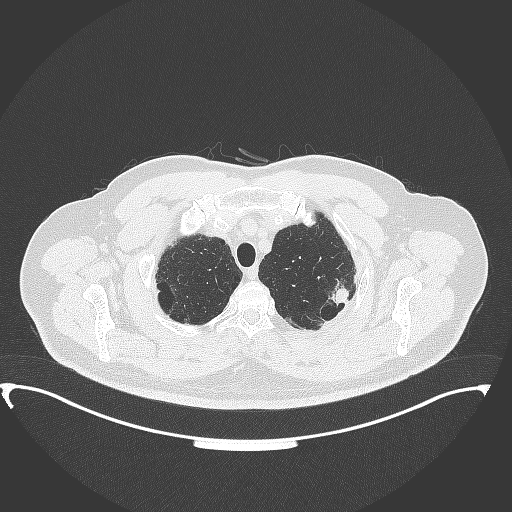
Chest CT, one axial slice. Slice 317 of 350 in the series (ordered by position). 120 kVp. Lung window (W 1500 / L -600 HU). 1 mm slice thickness. 512 × 512 image matrix. Patient: male, 64 years. From the clinical record (not read from this slice): clinical TNM (as recorded): T1c N1 M1.
Structures marked on this image (bounding box drawn by a radiologist):
- lung tumour (recorded histology: adenocarcinoma): box from (x=330, y=285) to (x=356, y=309) px